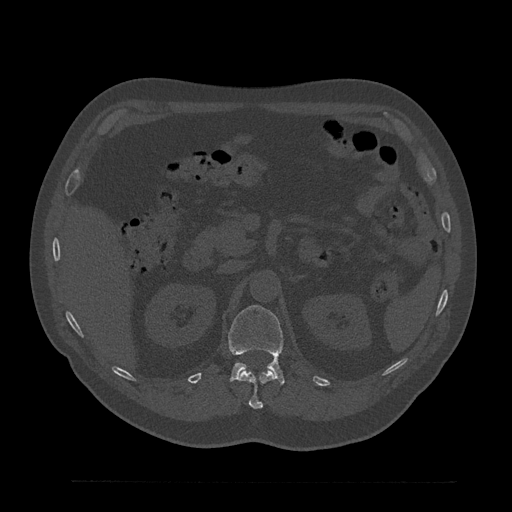
CT including the spine, one axial slice. Slice 192 of 797 in the series (ordered by position). 120 kVp. Bone window (W 1800 / L 400 HU). 0.5 mm slice thickness. 512 × 512 image matrix, field of view 430 × 430 mm. Male patient, age 61 years. Case-level facts recorded for this patient, not image findings: primary cancer: prostate.
Structures marked on this image (semi-automatic segmentation, software-assisted and operator-edited):
- L1 vertebra: bounding box <228,305,284,384> (left, top, right, bottom; pixels)
- T12 vertebra: <238,369,276,409>